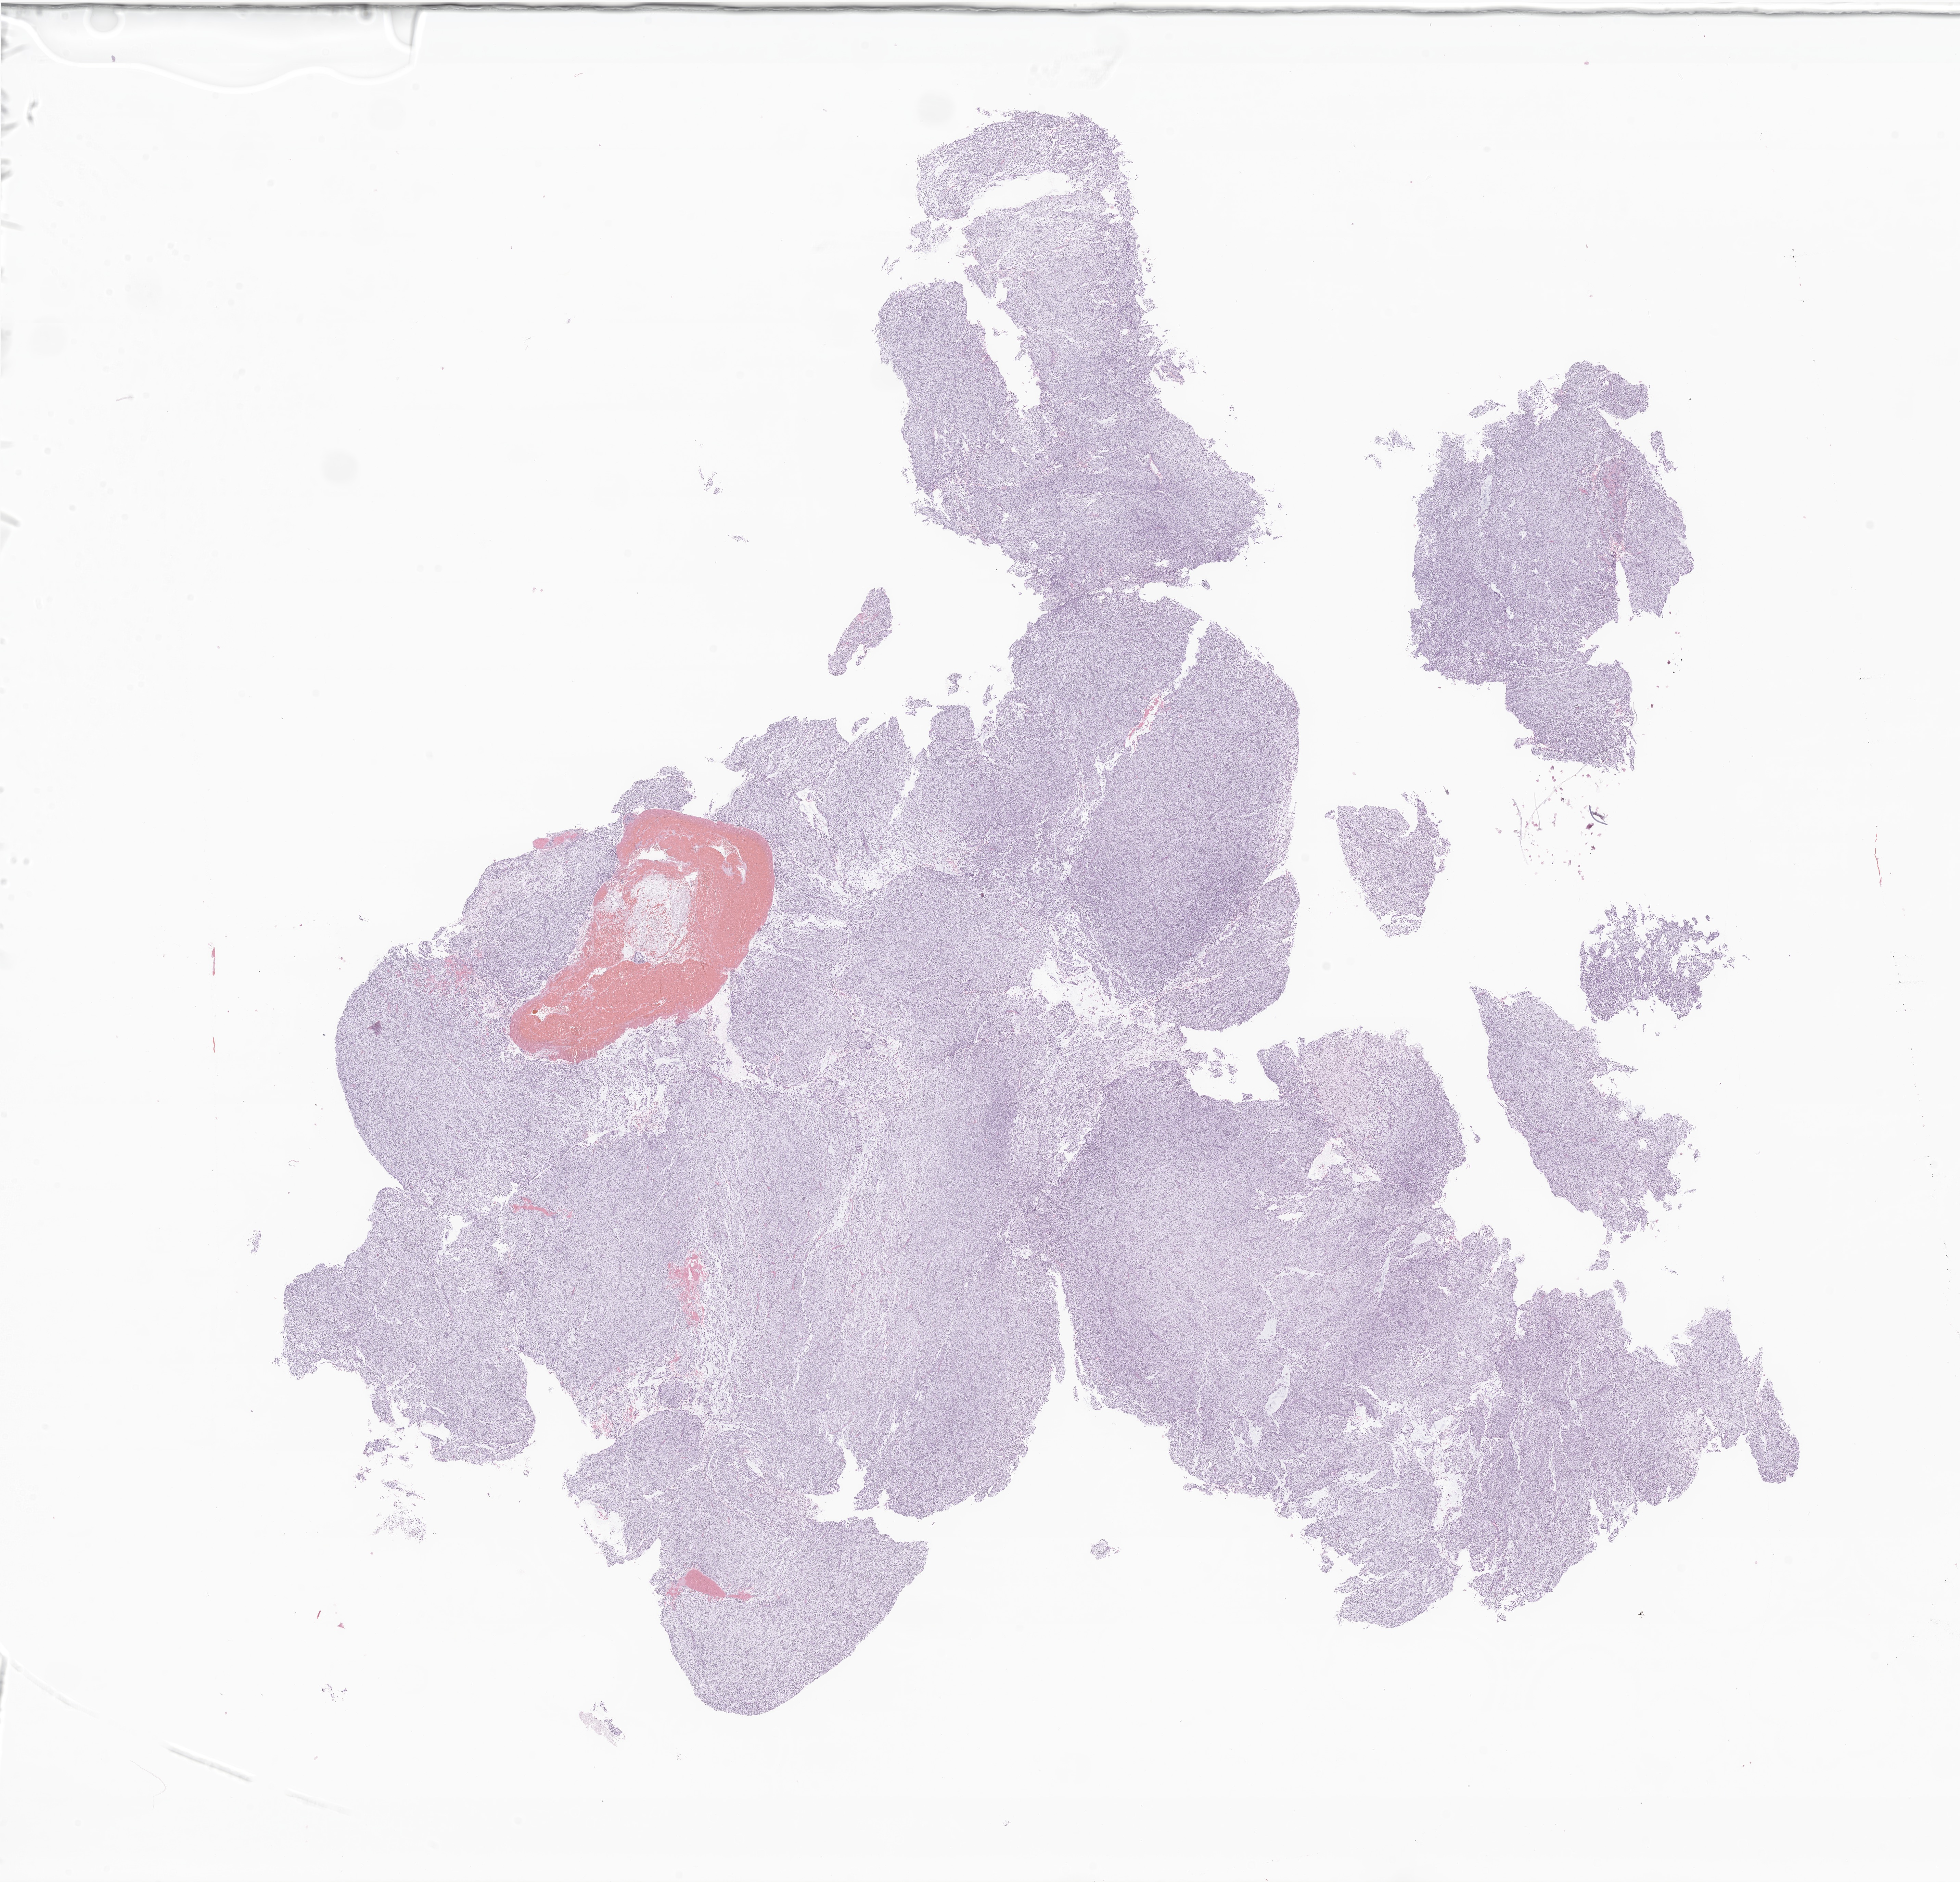
Whole-slide image, H&E stain of tumor tissue from the soft tissue of lower extremity — low-resolution overview of the scanned area, about 24.1 x 23.2 mm; FFPE section. Patient: female, age 131 months (10 years 11 months).
Tissue or organ of origin (case record): connective, subcutaneous and other soft tissues of lower limb and hip. Diagnosis: Sarcoma, NOS.